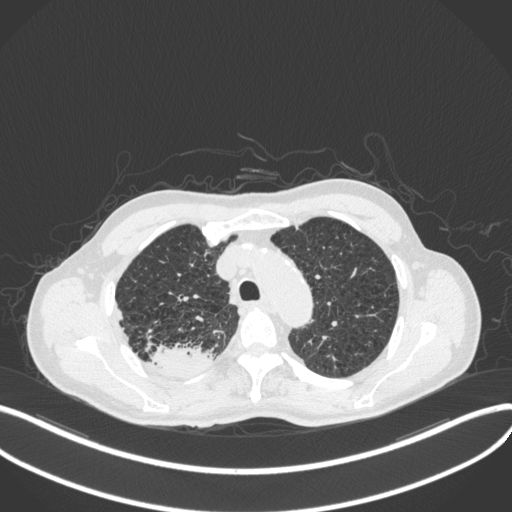
Chest CT, one axial slice; position 341 of 423 along the scan axis; 120 kVp; lung window (W 1500 / L -600 HU); 1 mm slice thickness; 512 × 512 image matrix. Male patient, age 79 years. Case-level facts recorded for this patient, not image findings: clinical TNM (as recorded): T3 N0 M0.
Structures marked on this image (bounding box drawn by a radiologist):
- lung tumour (recorded histology: adenocarcinoma): bounding box [x1, y1, x2, y2] px = [147, 340, 216, 382]